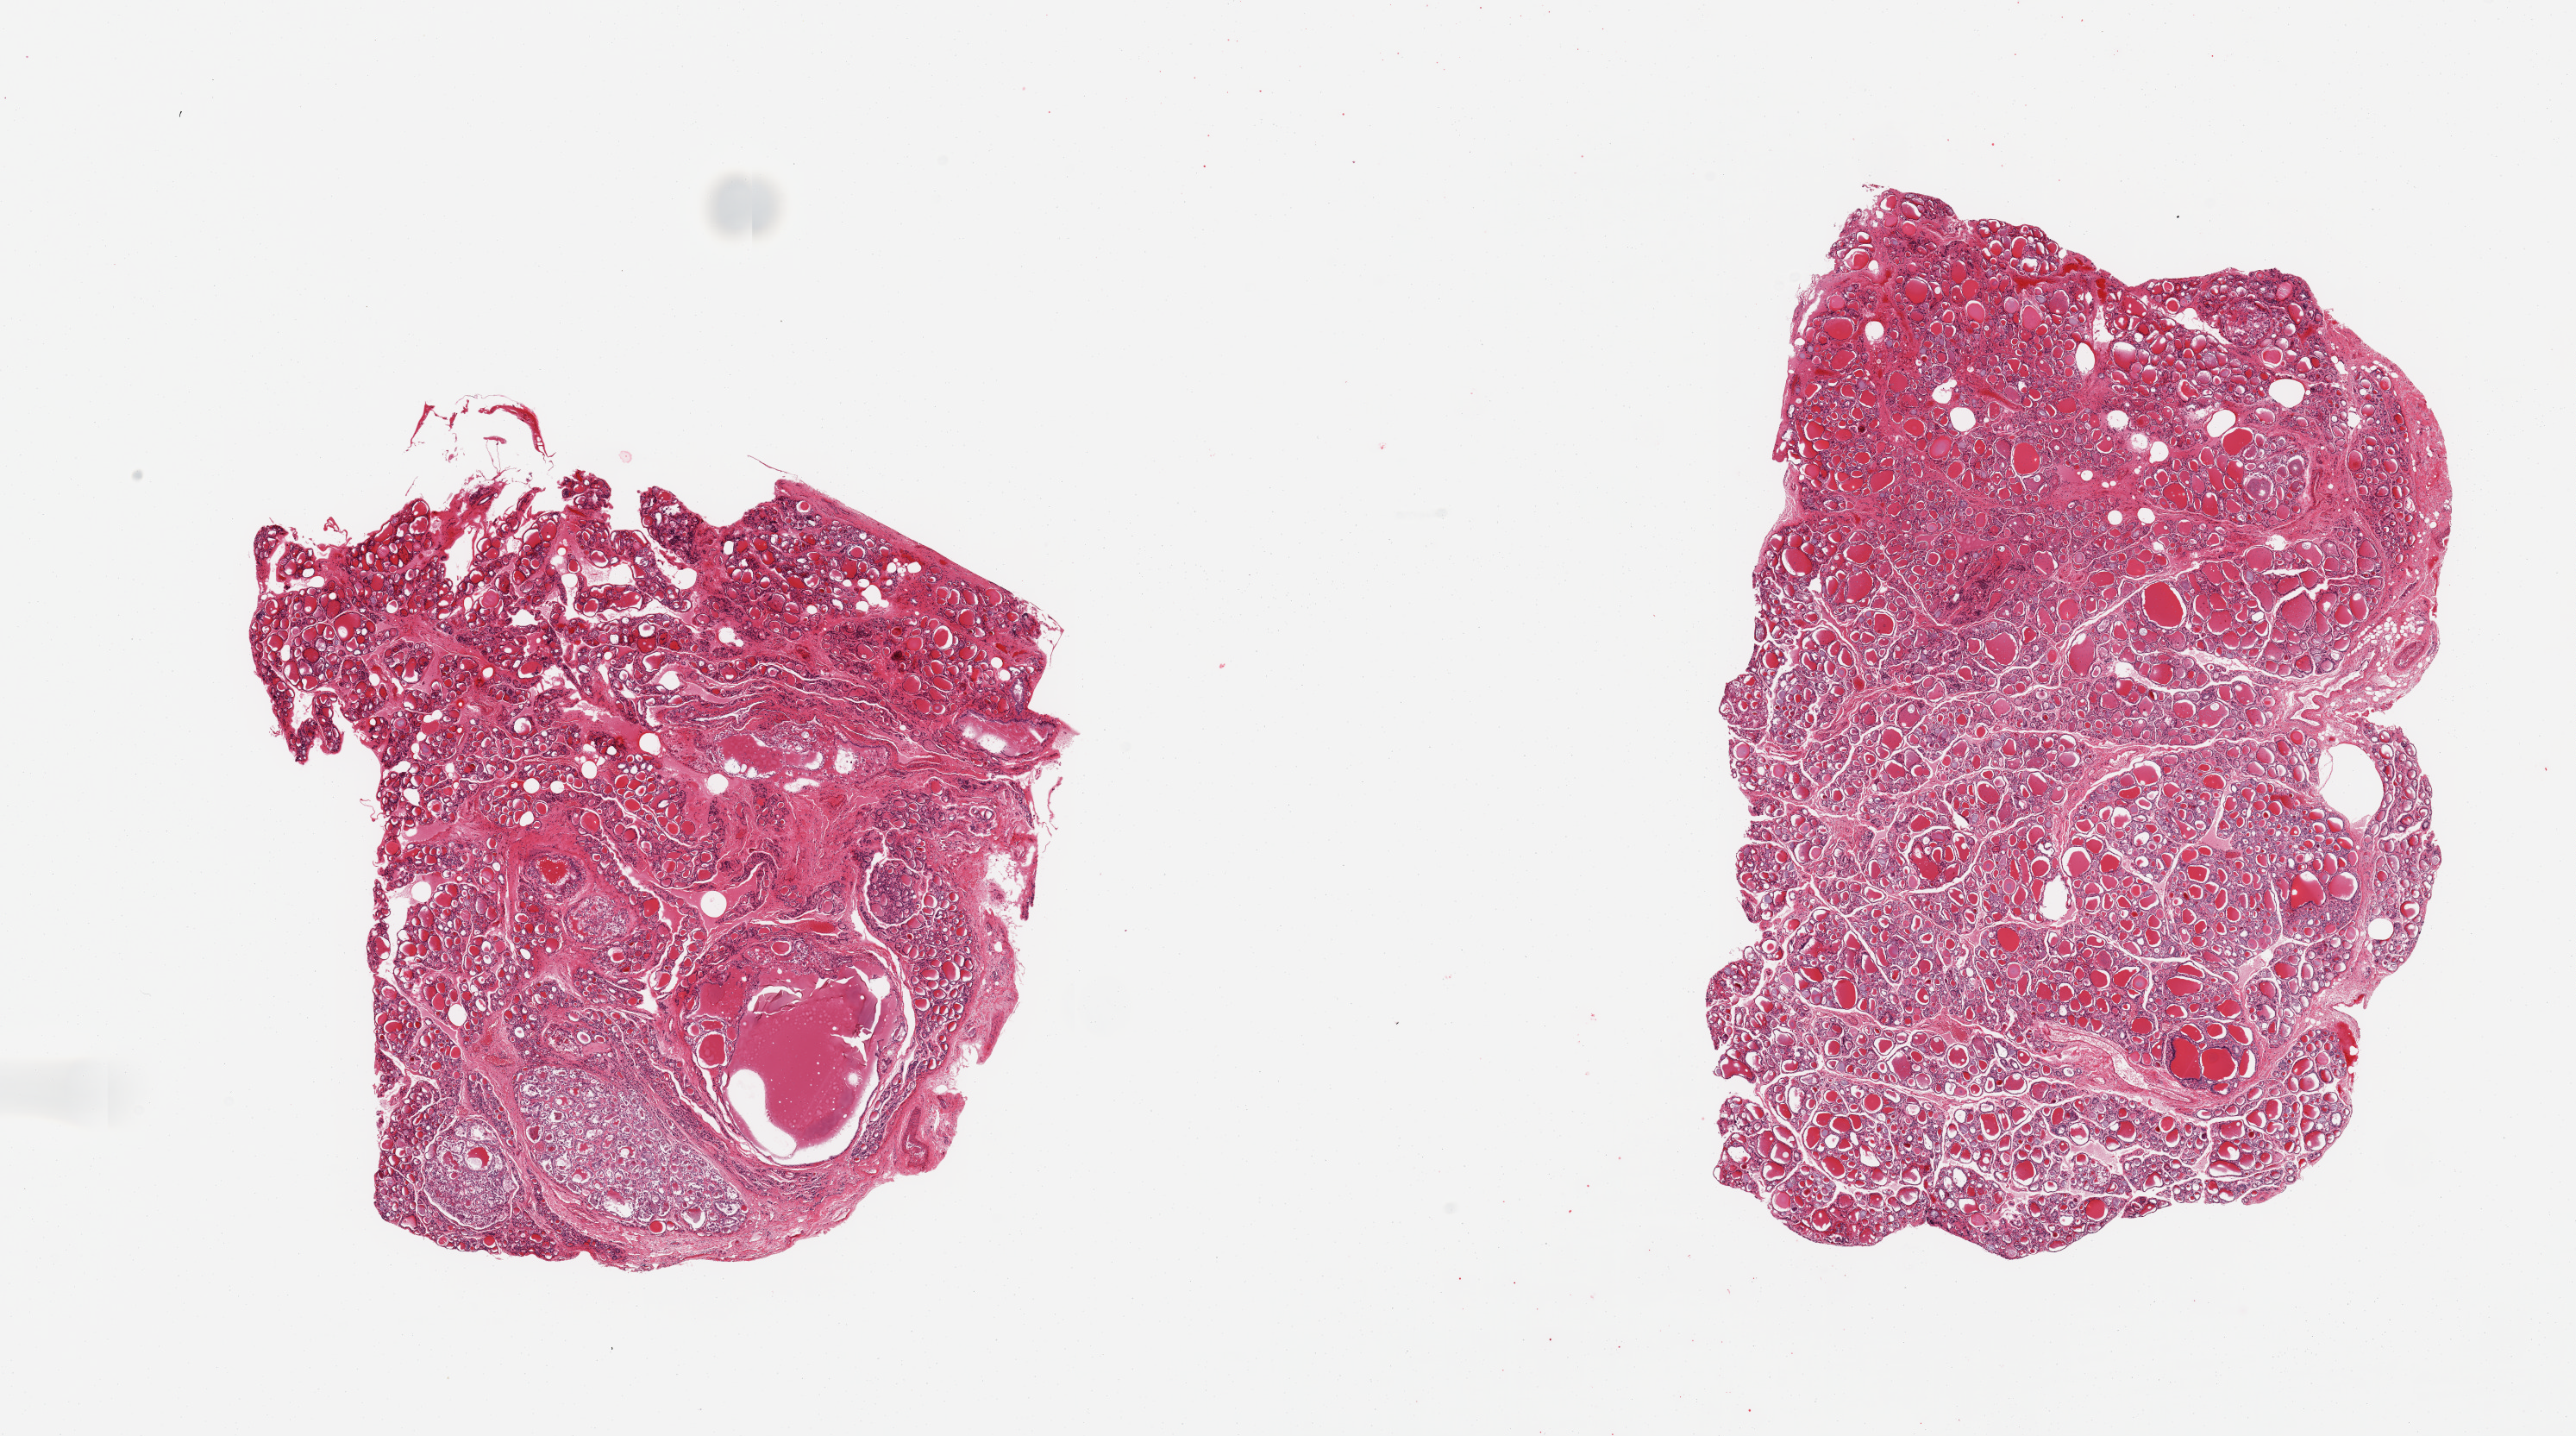
Digitized haematoxylin and eosin-stained section, a low-resolution overview of the entire scanned area, about 23.6 x 13.2 mm (from a 20x scan). PAXgene-fixed, paraffin-embedded tissue. Sampled site (target tissue): thyroid. Donor tissue sample.
Reviewer comment on this tissue sample: 2 pieces; nodular, especially in 1 piece.